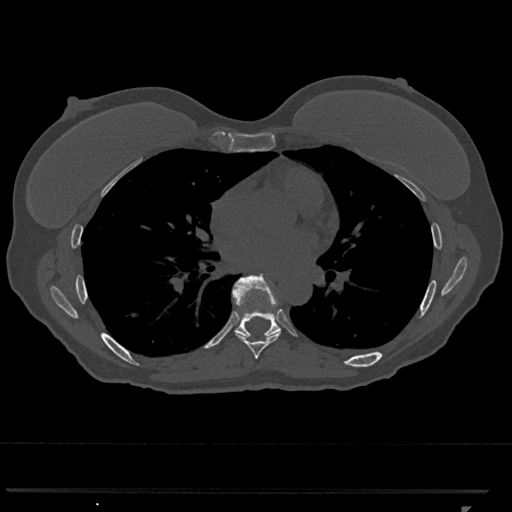
CT including the spine, one axial slice. Position 693 of 793 along the scan axis. Bone window (W 1800 / L 400 HU). 0.5 mm slice thickness. 512 × 512 image matrix. Female patient, age 62 years. Case-level facts recorded for this patient, not image findings: primary cancer: renal.
Annotated regions visible in this slice (semi-automatic segmentation, software-assisted and operator-edited):
- T7 vertebra: bounding box [x1, y1, x2, y2] px = [234, 331, 281, 359]
- T8 vertebra: [233, 274, 281, 337]